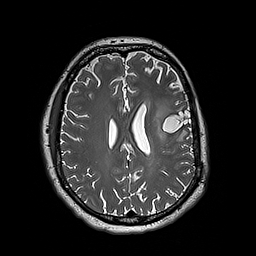
Brain MRI from a brain-tumour surgery series, one axial slice; slice 81 of 192 in the series (ordered by position); 1 mm slice thickness; 256 × 256 image matrix. From the clinical record (not read from this slice): histopathology: Astrocytoma; WHO grade: 3; IDH mutation: yes; tumour location: Left Insular.
Annotated regions visible in this slice (outlined manually by an expert reader):
- tumour: box from (x=152, y=97) to (x=176, y=144) px